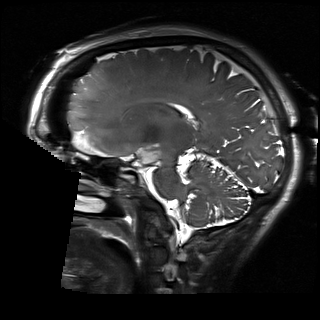
Brain MRI from a brain-tumour surgery series, one sagittal slice; position 109 of 192 along the scan axis; 1 mm slice thickness; 320 × 320 image matrix. From the clinical record (not read from this slice): histopathology: Glioblastoma; WHO grade: 2.
Annotated regions visible in this slice (outlined manually by an expert reader):
- residual tumour: box from (x=139, y=150) to (x=159, y=164) px